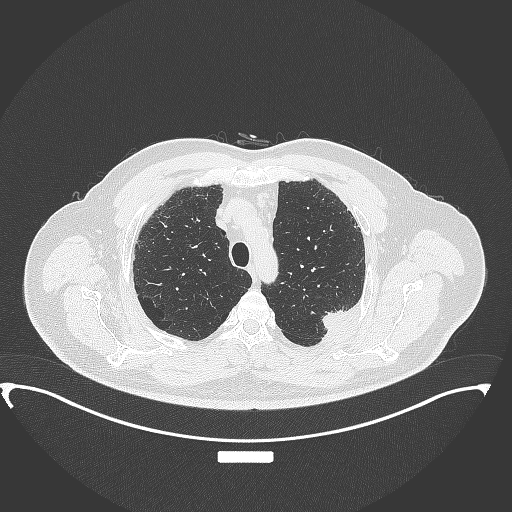
Chest CT, one axial slice. Position 287 of 350 along the scan axis. Reconstruction kernel B70f. 120 kVp. Lung window (W 1500 / L -600 HU). 512 × 512 image matrix, field of view 459 × 459 mm. Male patient, age 64 years. From the clinical record (not read from this slice): clinical TNM (as recorded): T1c N1 M1.
Annotated regions visible in this slice (rectangle marked by the reading radiologist):
- lung tumour (recorded histology: adenocarcinoma): bounding box [x1, y1, x2, y2] px = [317, 302, 355, 336]